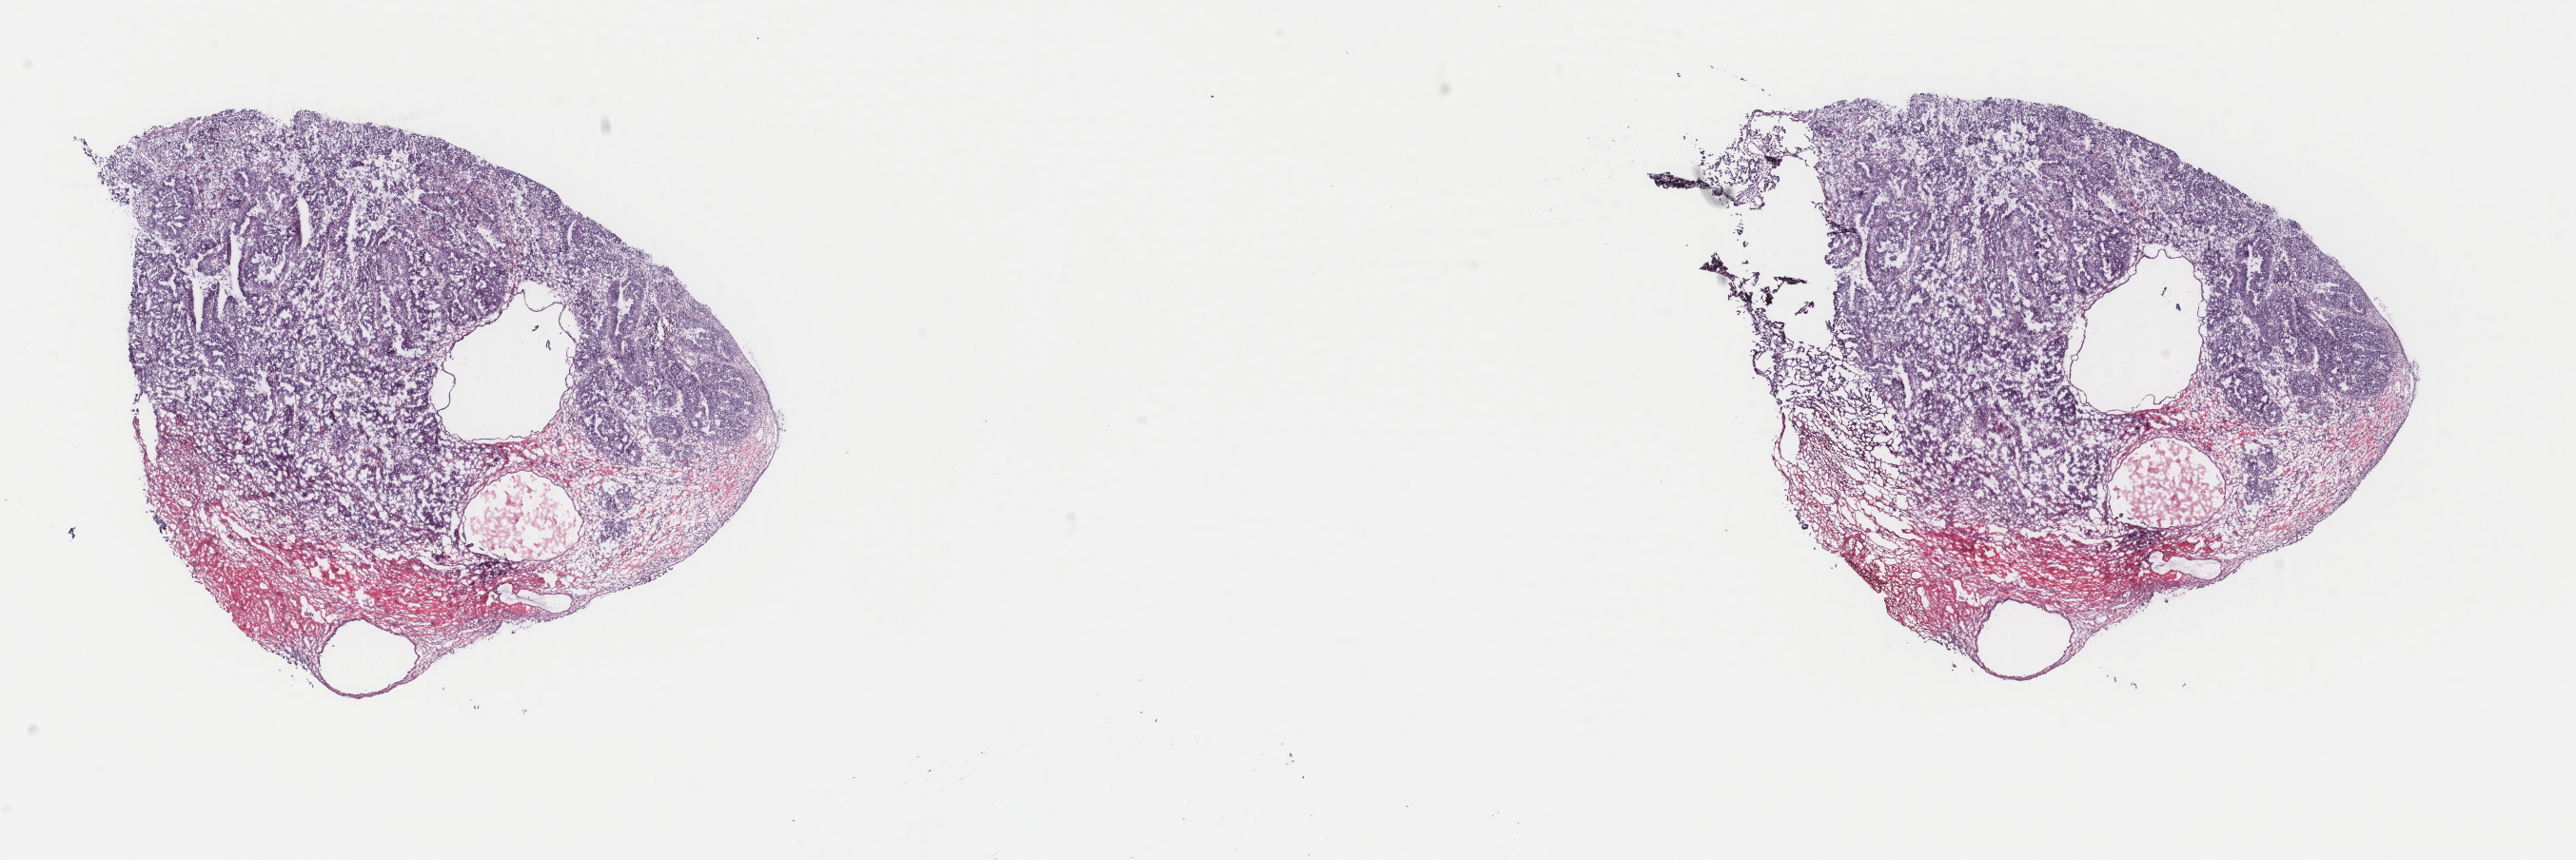
Hematoxylin and eosin (H&E) stained whole-slide image — low-resolution overview of the scanned area, about 21.5 x 7.2 mm (acquisition: 40x scan); frozen section; sample: primary tumour, uterus. Female, age 72 years at initial diagnosis. Histologic grade: G3 (poorly differentiated). Composition of this section per pathologist review: tumour cells 80%, tumour nuclei 90%, normal cells 20%, stromal cells 0%, necrosis 0%. Inflammatory infiltration, as recorded: lymphocyte infiltration 1%, monocyte infiltration 0%, neutrophil infiltration 0%.
* FIGO stage: IA
* pathologic diagnosis: Serous cystadenocarcinoma, NOS (endometrium)